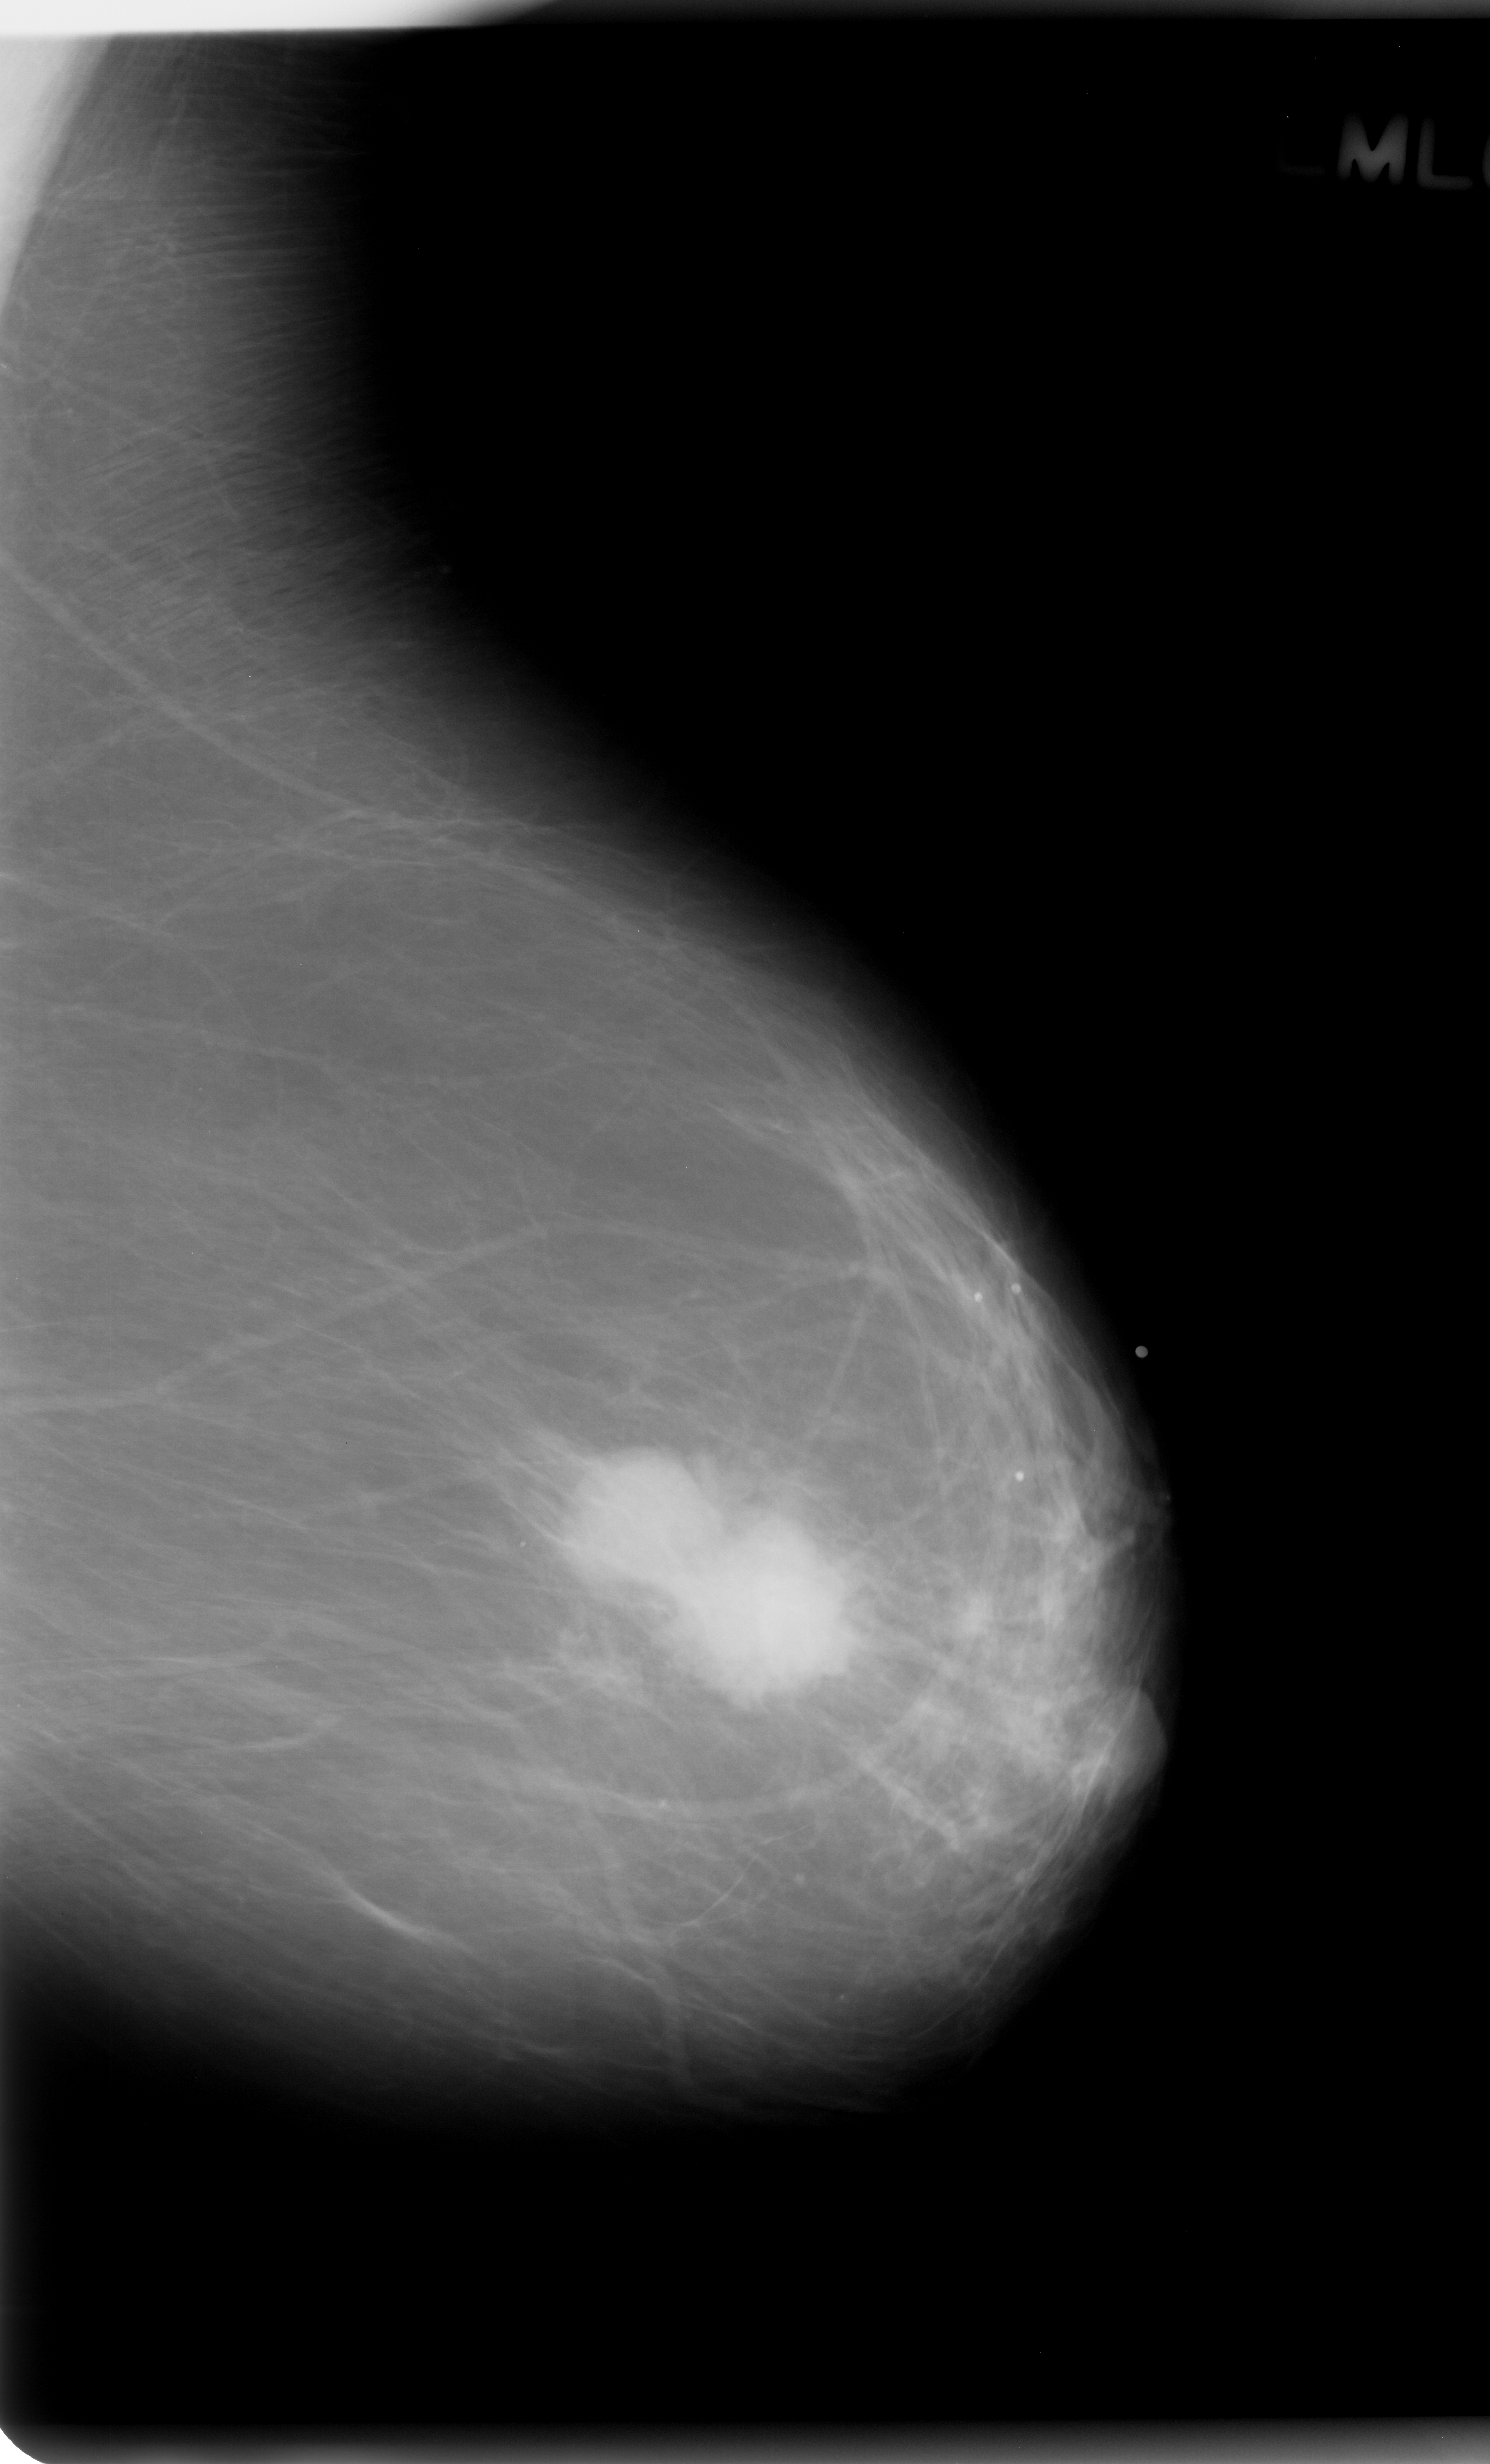
Scanned film-screen mammogram; left breast; mediolateral oblique (MLO) view.
Mass, shape lobulated, margins microlobulated; BI-RADS assessment category 5; subtlety rating 5 on a 1 (subtle) to 5 (obvious) scale; pathology result (as recorded, not read from the image): malignant.